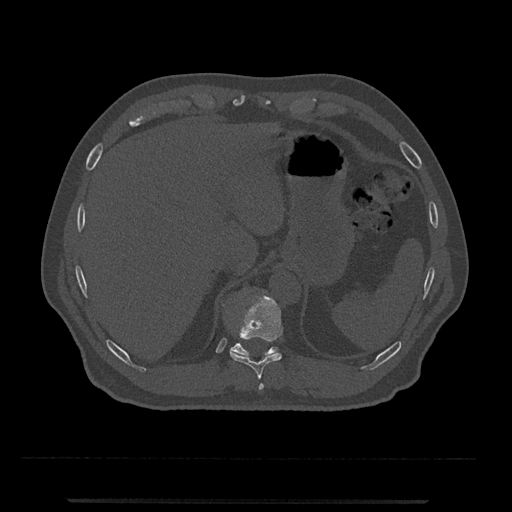
CT including the spine, one axial slice; slice 501 of 797 in the series (ordered by position); reconstruction kernel Br40s/3; 120 kVp; bone window (W 1800 / L 400 HU); 0.5 mm slice thickness; 512 × 512 image matrix. Patient: male, 63 years. From the clinical record (not read from this slice): primary cancer: prostate.
Structures marked on this image (semi-automatically segmented with operator editing):
- T10 vertebra: bounding box [x1, y1, x2, y2] px = [230, 293, 283, 380]
- T11 vertebra: [230, 342, 278, 356]
- T9 vertebra: [259, 383, 264, 390]